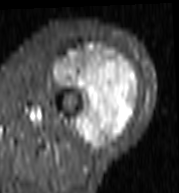
MRI of an extremity soft-tissue mass, one axial slice. STIR. MR volume resampled by the dataset authors to the PET/CT grid (not the native acquisition matrix). 3.27 mm slice thickness. 179 × 193 image matrix, field of view 175 × 188 mm. Female patient. Case-level facts recorded for this patient, not image findings: histological type: undifferentiated – high grade; grade: high; site of the primary tumour: left thigh.
Structures marked on this image (expert contour drawn on MRI and transferred to this co-registered scan by the dataset authors):
- gross tumour volume including surrounding oedema: bounding box [x1, y1, x2, y2] px = [50, 44, 140, 150]
- gross tumour volume (mass): [54, 46, 138, 150]